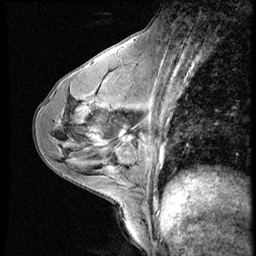
Breast MRI (dynamic contrast-enhanced), one sagittal slice; slice 33 of 56 in the series (ordered by position); dynamic contrast-enhanced series, image 2 of 4 at this slice position (ordered by acquisition); 1.5 T; TE 4.2 ms, TR 9 ms; 256 × 256 image matrix. Patient: female, 43 years. Case-level facts recorded for this patient, not image findings: setting: breast cancer imaged before/during neoadjuvant chemotherapy; receptor status: HR-positive, HER2-negative.
Structures marked on this image (semi-automatic segmentation, software-assisted and operator-edited):
- analysis volume of interest (the breast-tissue region the enhancement analysis was run in; not a lesion): box from (x=104, y=104) to (x=152, y=159) px
- tumour enhancement mask (voxels above the 140 % enhancement threshold inside the analysis volume of interest): (x=120, y=130)–(x=130, y=141)